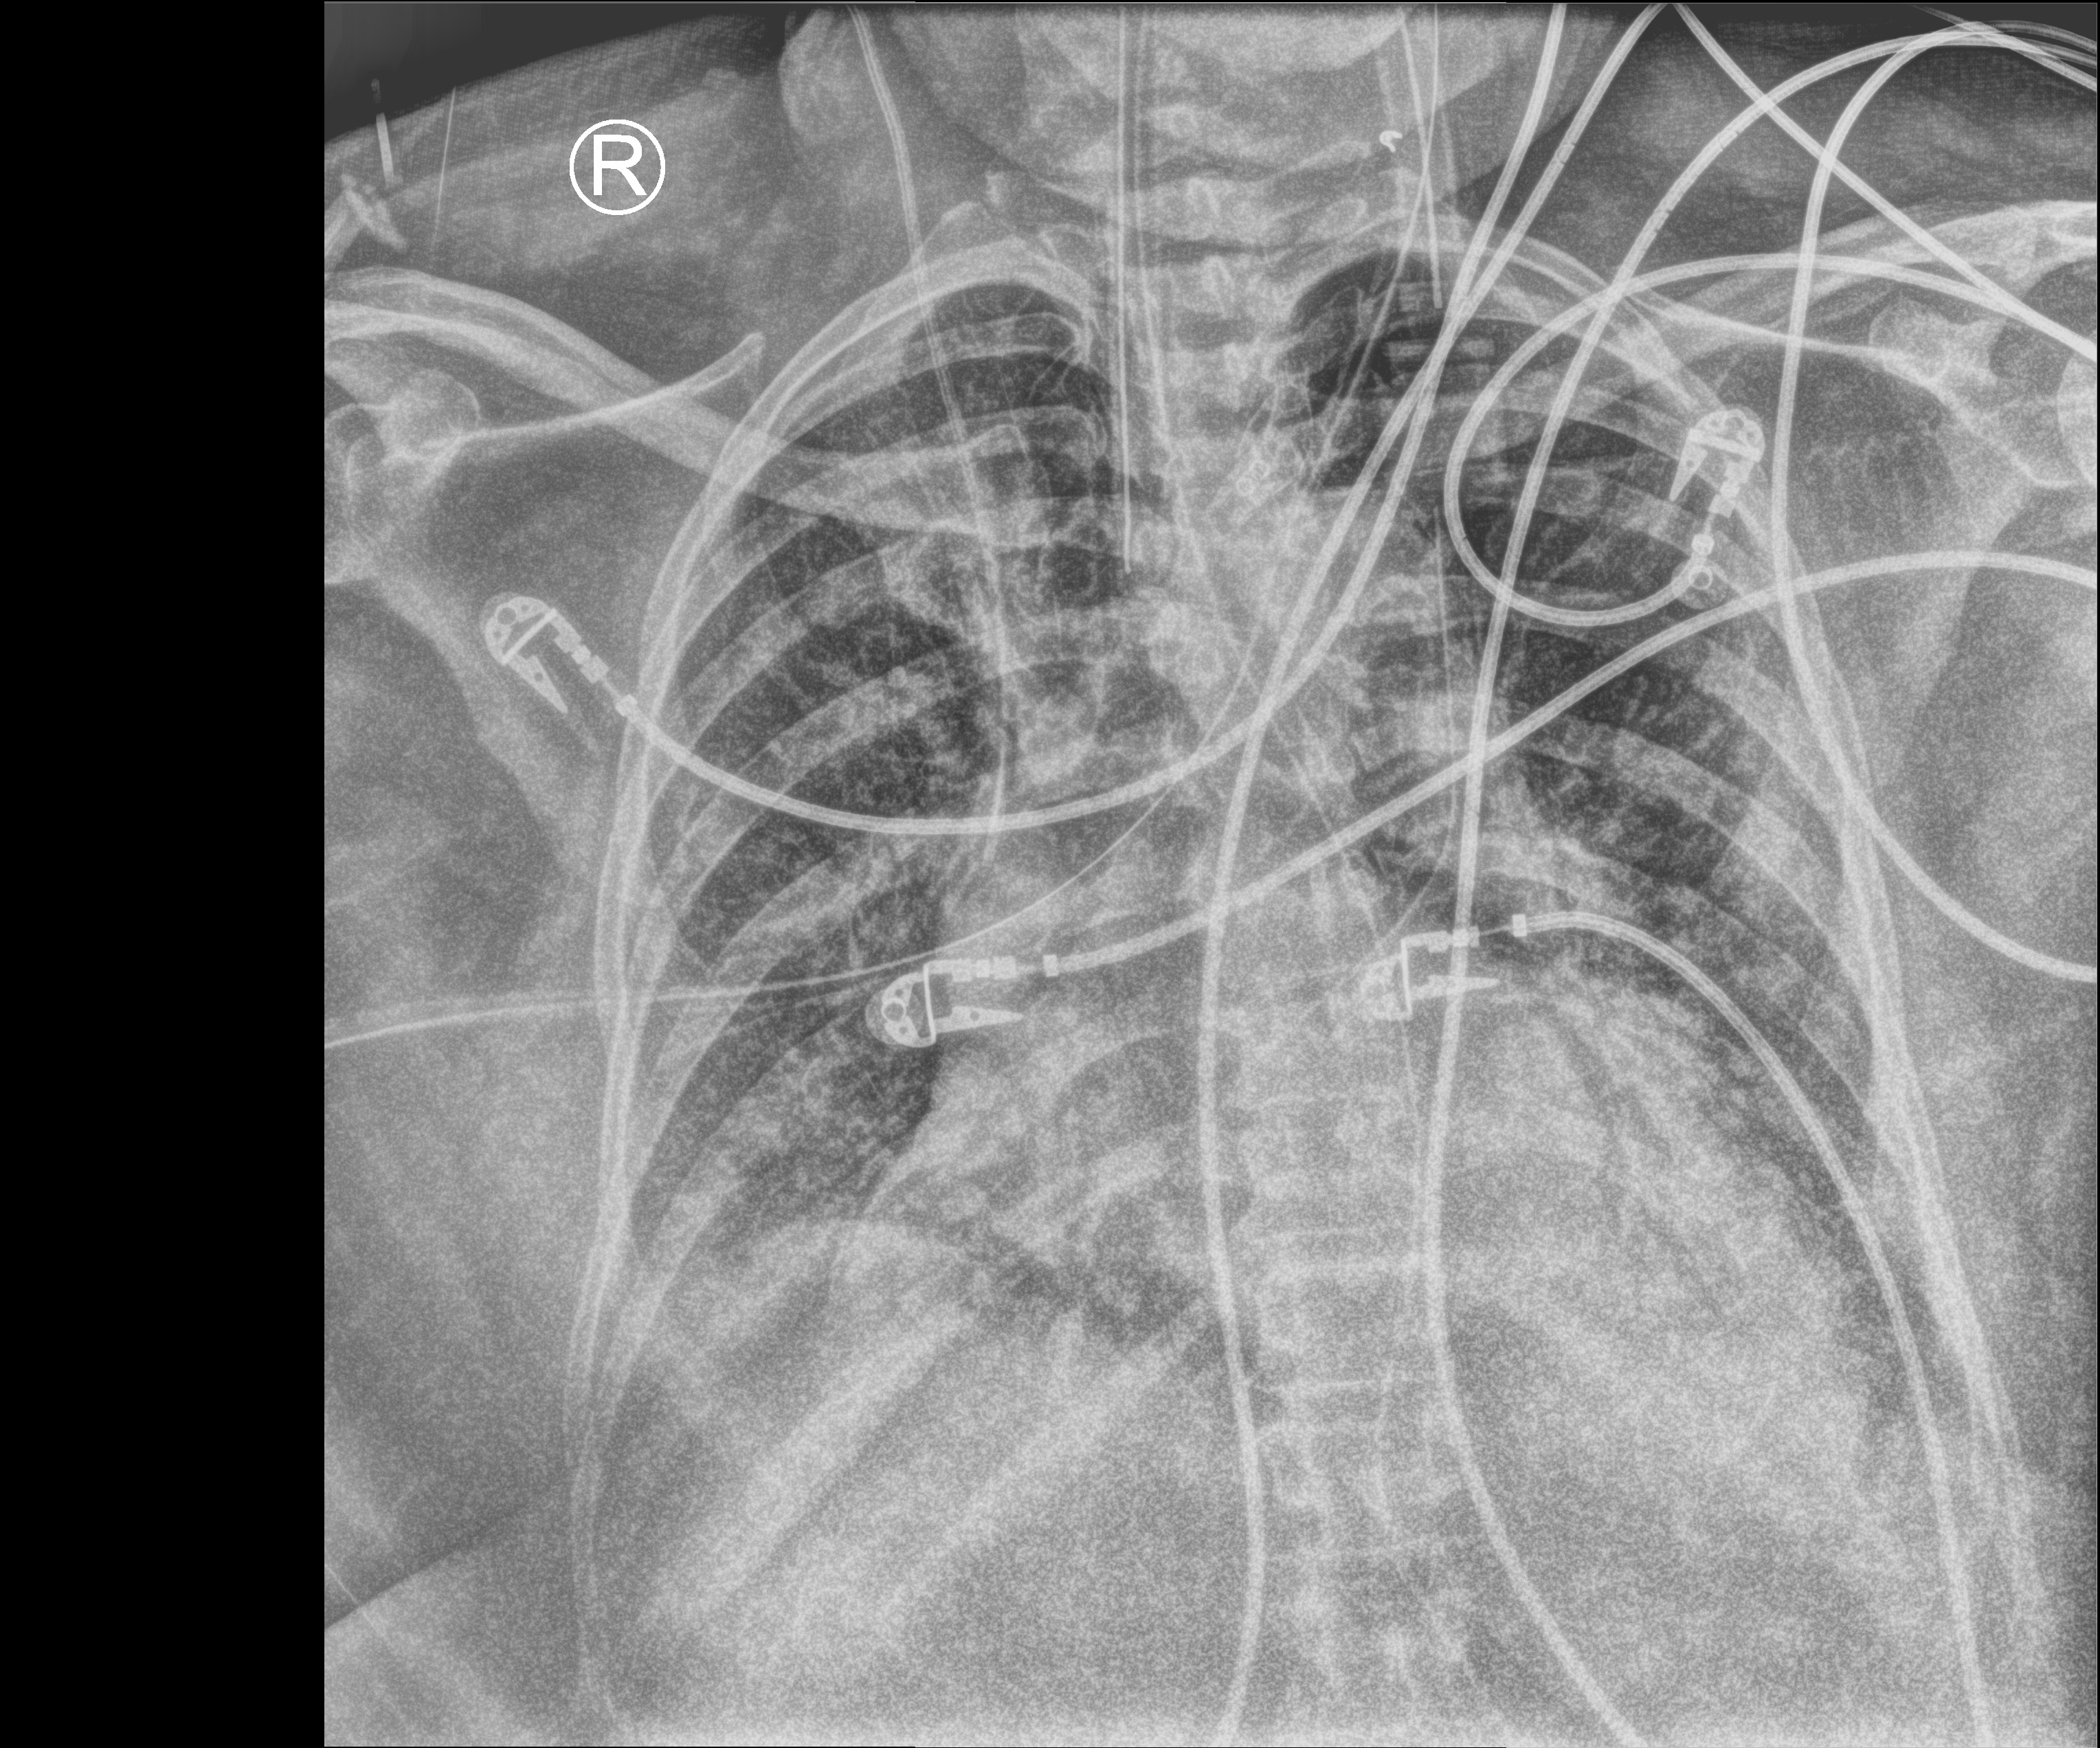
Bedside chest radiograph (computed radiography); anteroposterior (AP) projection. Female patient hospitalised with COVID-19, age 60–74 years.
From the hospital-stay record, not from the radiograph (when in the stay this image was taken is not recorded): mechanically ventilated during this hospital stay: yes.